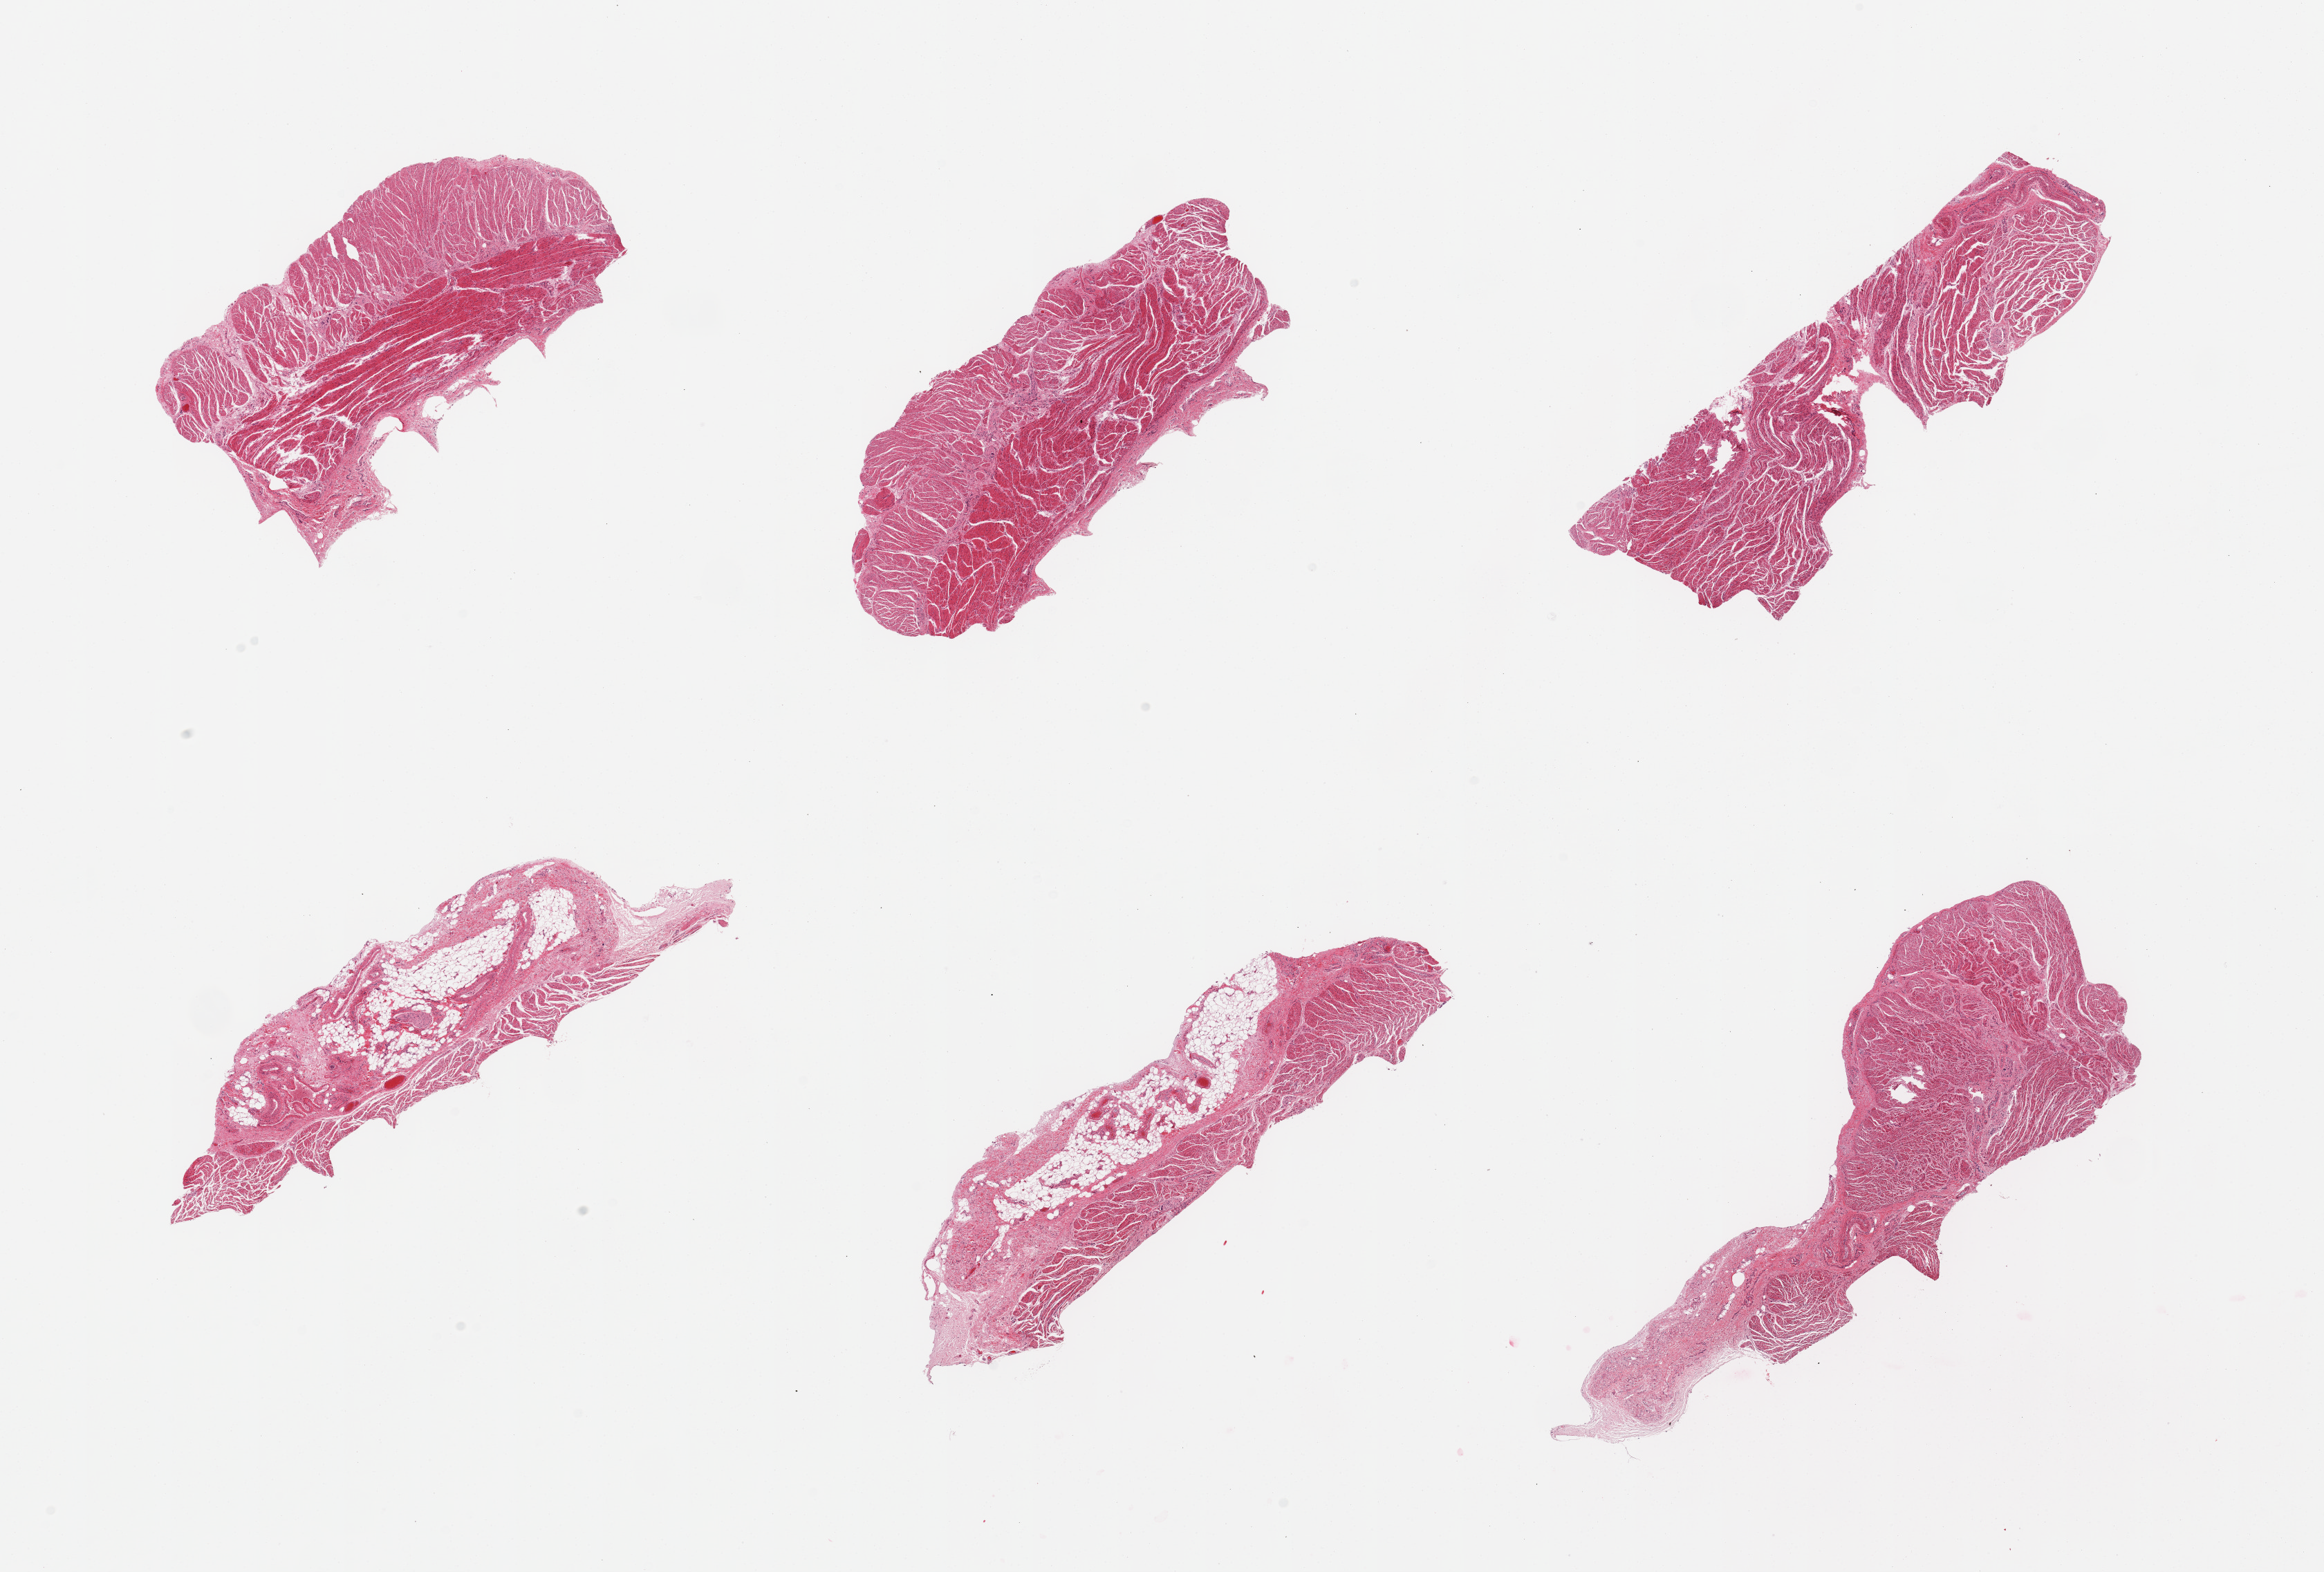
Hematoxylin and eosin (H&E) whole-slide image, brightfield — shown as a low-resolution overview of the whole scanned area (about 26.6 x 18.0 mm). PAXgene-fixed paraffin-embedded (PFPE) section. Target tissue: gastroesophageal junction. Donor tissue sample.
Reviewer comment on this tissue sample: 6 pieces; 2 pieces include significant fat, nerve, vessels.